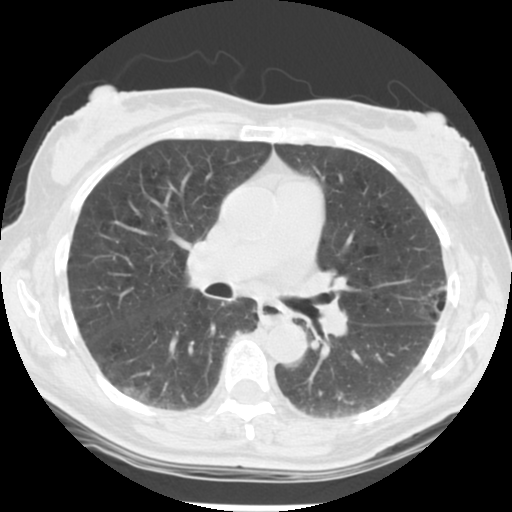
Low-dose screening chest CT, one axial slice. Reconstruction kernel STANDARD. 120 kVp. Lung window (W 1500 / L -600 HU). 2.5 mm slice thickness. 512 × 512 image matrix.
Outlined on this slice (expert manual segmentation):
- lesion 1 (tumor, upper lobe of left lung): bounding box (x1, y1, x2, y2) in pixels: (420, 284, 447, 319)